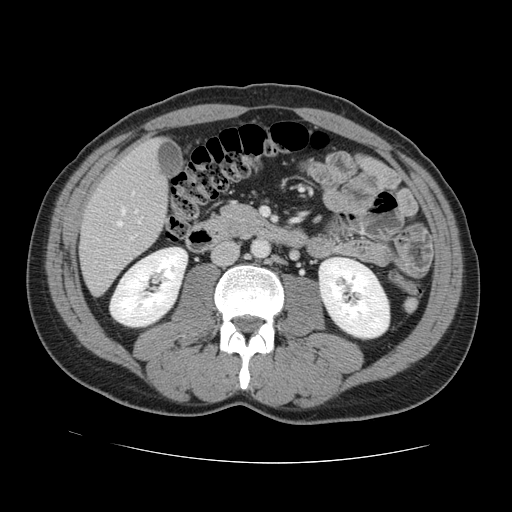
Contrast-enhanced abdominal CT, one axial slice; slice 41 of 131 in the series (ordered by position); 120 kVp; intravenous contrast given; soft-tissue window (W 400 / L 40 HU); 2.5 mm slice thickness; 512 × 512 image matrix, field of view 380 × 380 mm. Male patient, age 40 years. Case-level facts recorded for this patient, not image findings: diagnosis: colorectal cancer liver metastases, imaged before liver resection; multiple liver metastases: yes; largest metastasis: 2.9 cm; disease in both lobes: yes.
Outlined on this slice (expert manual segmentation):
- hepatic veins: bounding box [x1, y1, x2, y2] px = [117, 209, 140, 226]
- liver: [81, 141, 168, 294]
- planned liver remnant (the part of the liver to remain after resection): [132, 142, 158, 163]
- portal vein (with intrahepatic branches): [130, 192, 135, 239]